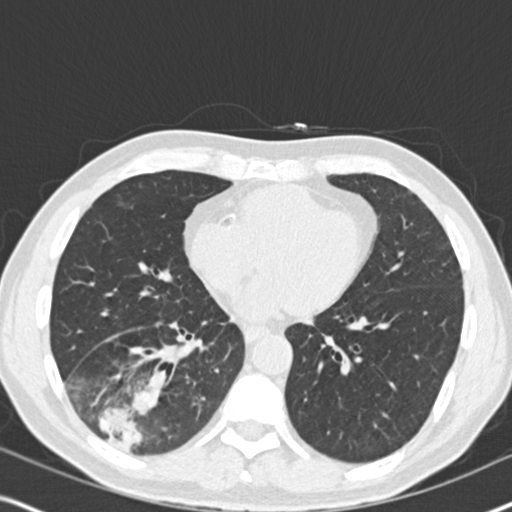
Low-dose screening chest CT, one axial slice; slice 80 of 182 in the series (ordered by position); reconstruction kernel B30f; lung window (W 1500 / L -600 HU); 2 mm slice thickness; 512 × 512 image matrix, field of view 330 × 330 mm.
Structures marked on this image (outlined manually by an expert reader):
- lesion 1 (tumor, lower lobe of right lung): bounding box [x1, y1, x2, y2] px = [101, 386, 160, 449]